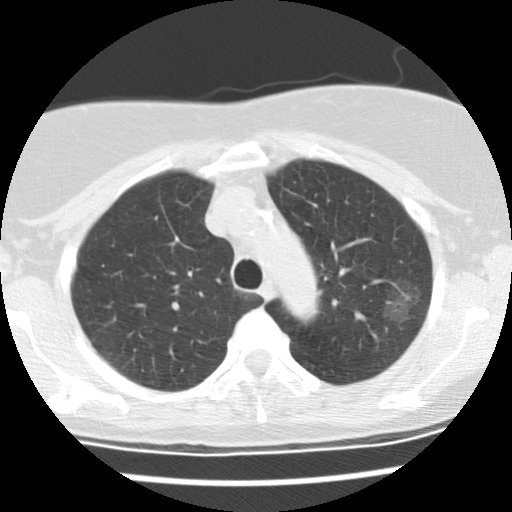
Low-dose screening chest CT, axial slice. First (baseline) screen. Lung window (W 1500 / L -600 HU). Slice 108 of 137 in the series. 512 × 512 image matrix. Female participant, aged 66 years at enrolment. Former smoker at enrolment.
Lesion marked by an expert reader, bounding box <381,278,425,323> (left, top, right, bottom; pixels). The exam's reader record, not a measurement of the box and not confirmed to be the same lesion: non-calcified nodule or mass ≥4 mm, left upper lobe, 25 × 17 mm, poorly defined margins, mixed attenuation. Official screen result: positive, change unspecified: nodule(s) >= 4 mm or enlarging nodule(s), mass(es), or other non-specific abnormalities suspicious for lung cancer. Participant outcome: lung cancer diagnosed 44 days after this screen — bronchiolo-alveolar adenocarcinoma, NOS, left upper lobe, well differentiated (G1), stage IA (AJCC 6th edition), 19 mm at pathology.